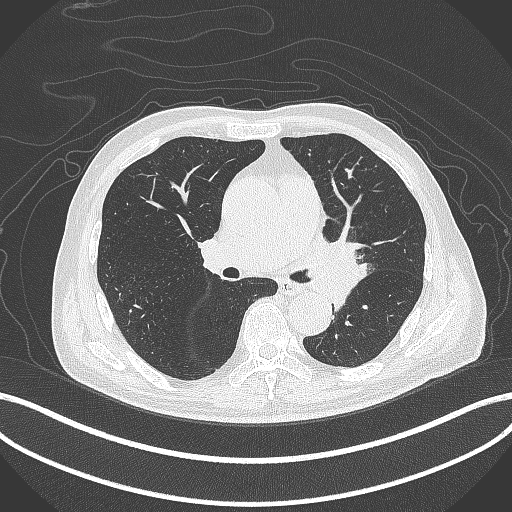
Chest CT, one axial slice. 120 kVp. Lung window (W 1500 / L -600 HU). 1 mm slice thickness. 512 × 512 image matrix, field of view 400 × 400 mm. Patient: male, 77 years. Case-level facts recorded for this patient, not image findings: clinical TNM (as recorded): T3 N1 M0.
Annotated regions visible in this slice (bounding box drawn by a radiologist):
- lung tumour (recorded histology: adenocarcinoma): bounding box [x1, y1, x2, y2] px = [301, 234, 370, 309]